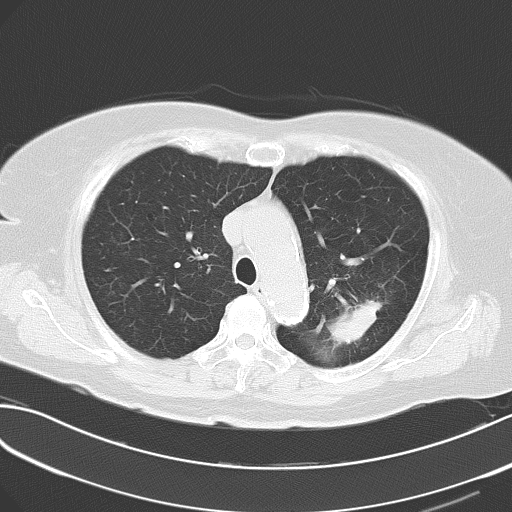
Chest CT, one axial slice. Position 50 of 62 along the scan axis. Lung window (W 1500 / L -600 HU). 512 × 512 image matrix. Patient: female, 70 years. Case-level facts recorded for this patient, not image findings: clinical TNM (as recorded): T2 N0 M0.
Annotated regions visible in this slice (rectangle marked by the reading radiologist):
- lung tumour (recorded histology: adenocarcinoma): bounding box [x1, y1, x2, y2] px = [325, 292, 380, 350]